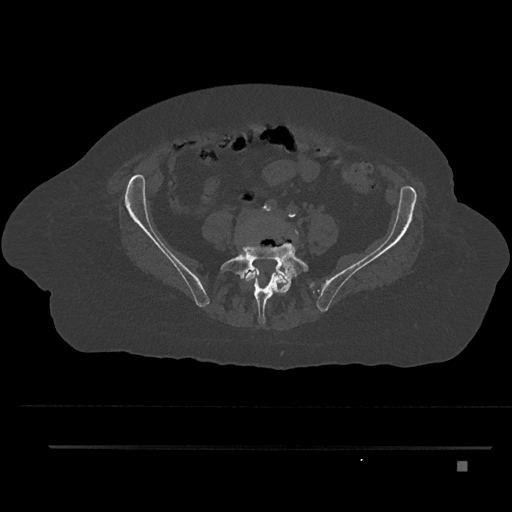
CT including the spine, one axial slice; slice 48 of 797 in the series (ordered by position); reconstruction kernel Br40s/3; 120 kVp; bone window (W 1800 / L 400 HU); 0.5 mm slice thickness; 512 × 512 image matrix. Patient: female, 76 years. Case-level facts recorded for this patient, not image findings: primary cancer: lung.
Structures marked on this image (semi-automatically segmented with operator editing):
- L4 vertebra: bounding box (x1, y1, x2, y2) in pixels: (240, 222, 298, 305)
- L5 vertebra: (220, 229, 309, 324)